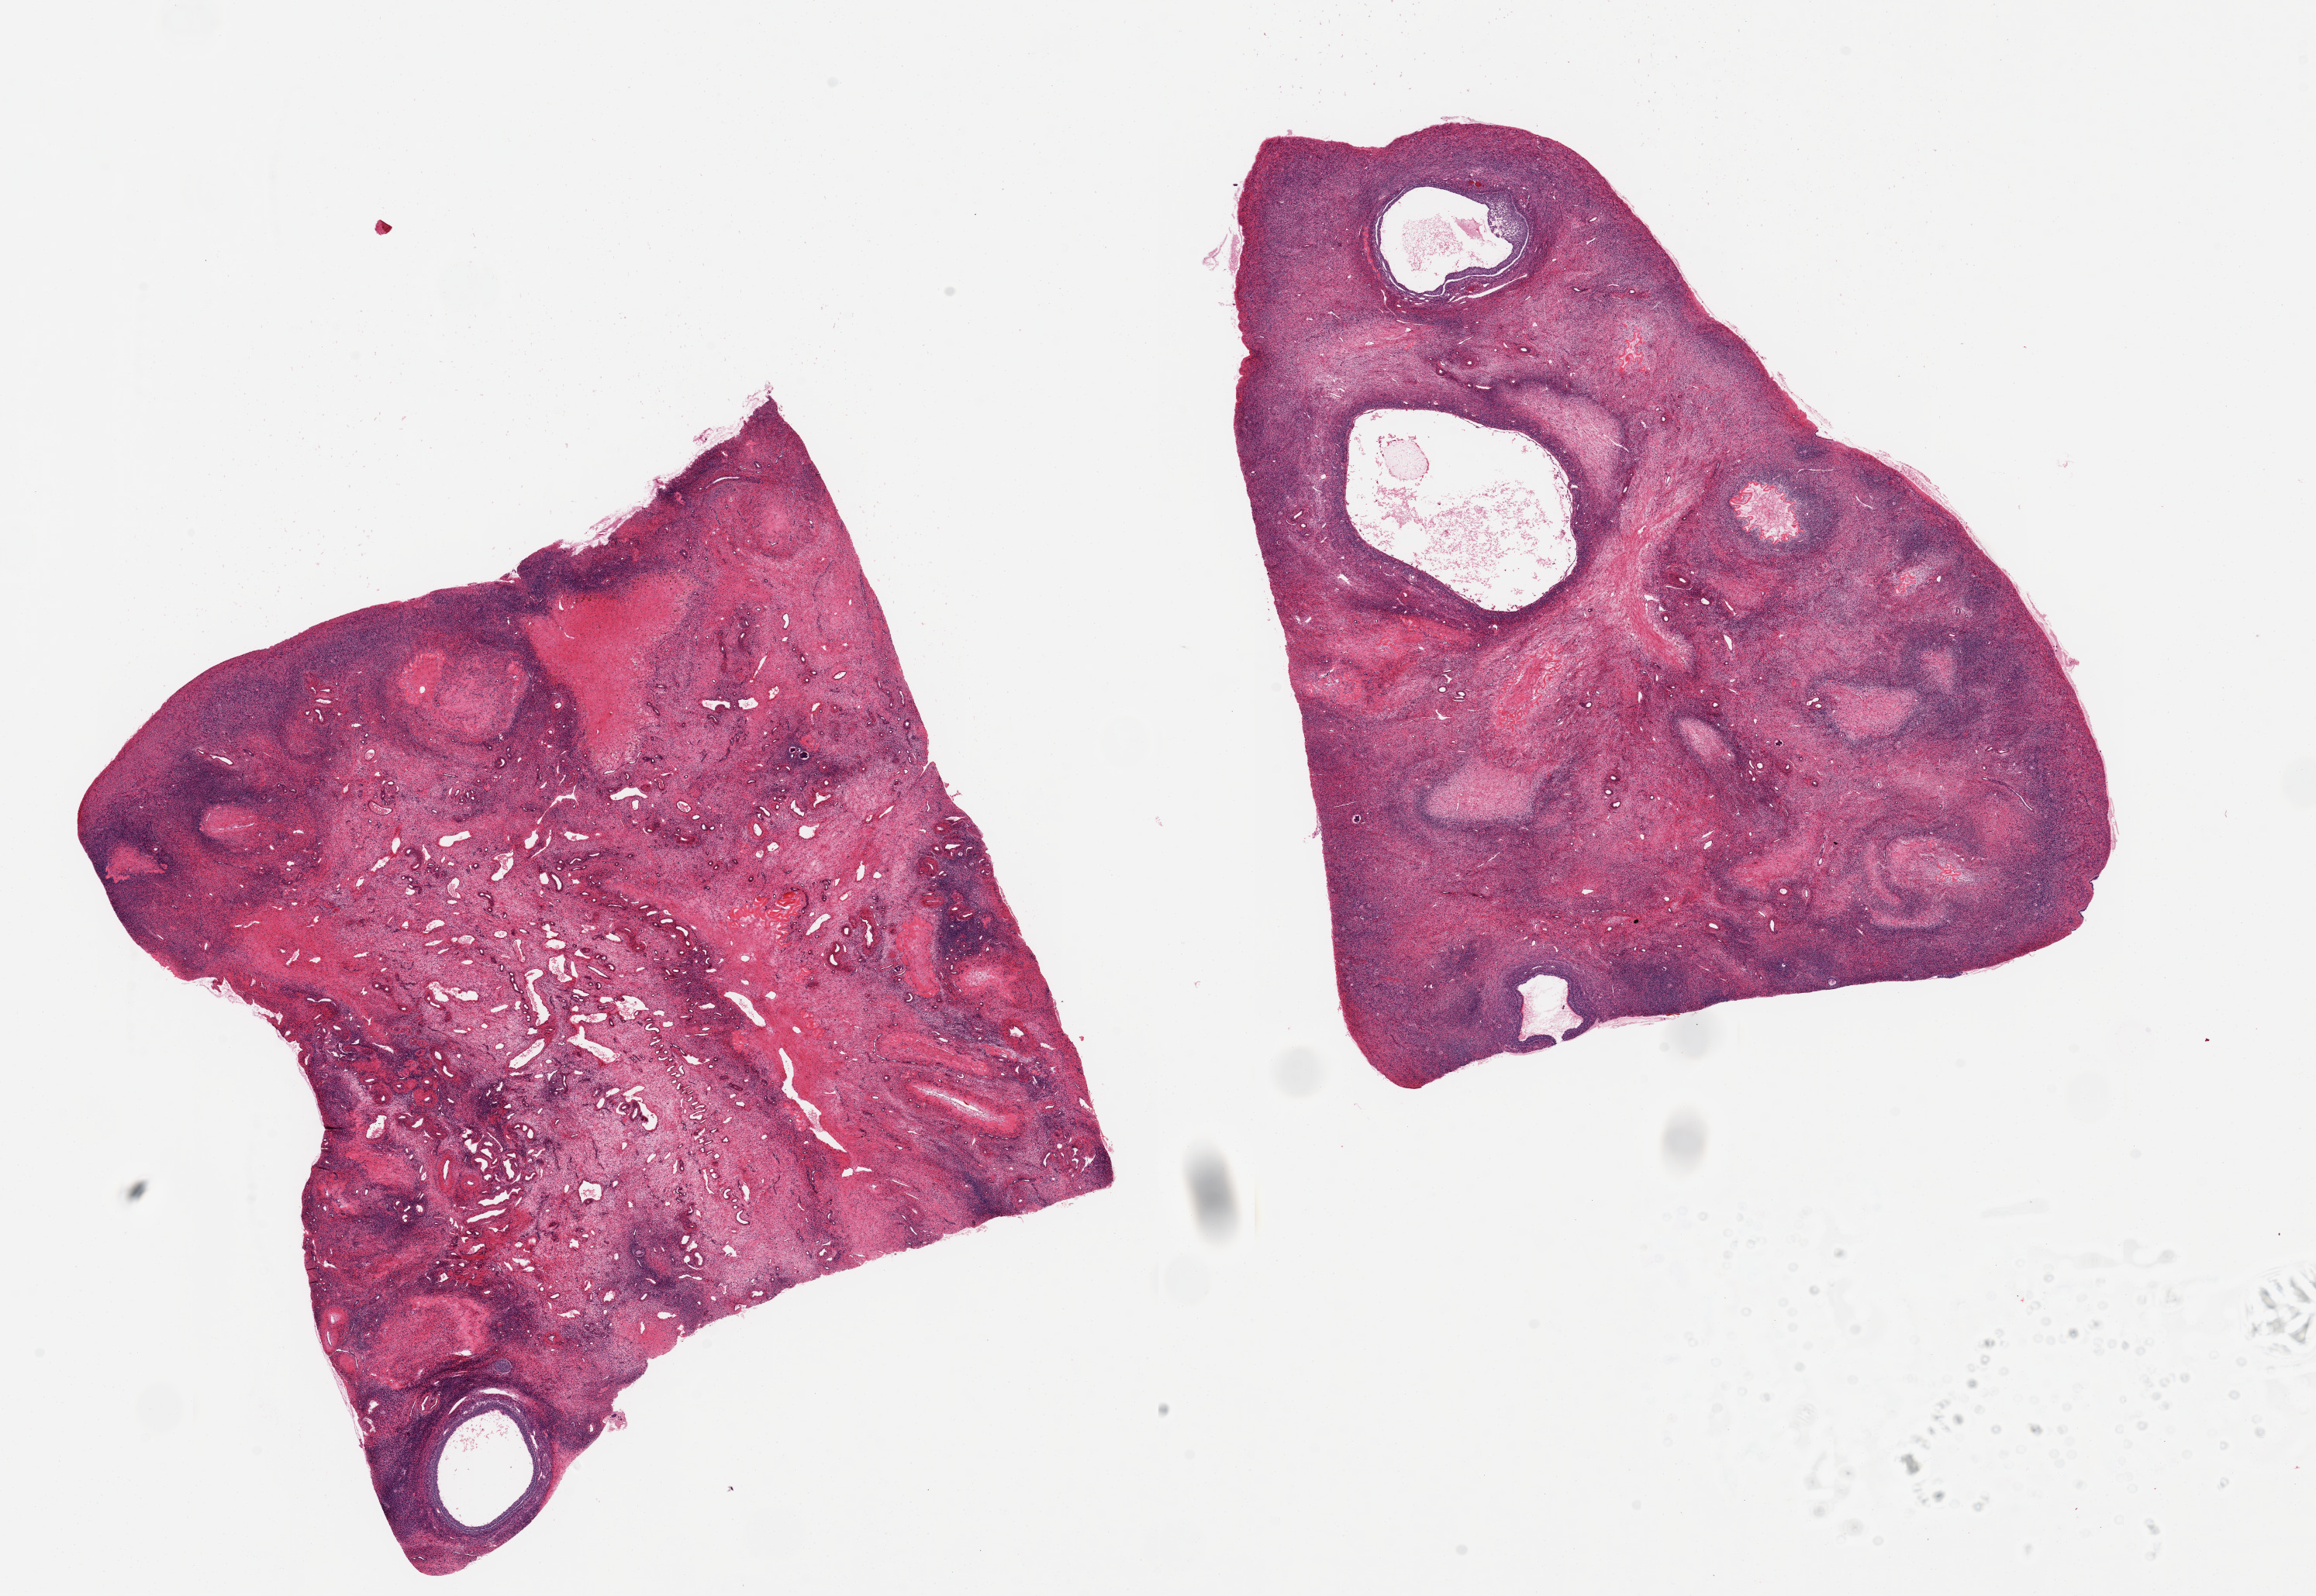
Whole-slide image, H&E stain — shown as a low-resolution overview of the whole scanned area (about 23.6 x 16.3 mm, slide scanned at 20x). PAXgene-fixed paraffin-embedded (PFPE) section. Target tissue: ovary. Donor tissue sample.
Reviewer comment on this tissue sample: 2 pieces, 10x8 & 9x8 mm; numerous ova and follicles present.